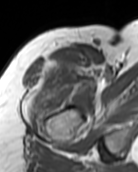
MRI of an extremity soft-tissue mass, one axial slice; position 82 of 99 along the scan axis; MR volume resampled by the dataset authors to the PET/CT grid (not the native acquisition matrix); 3.27 mm slice thickness; 138 × 172 image matrix. Female patient. From the clinical record (not read from this slice): histological type: pleiomorphic undifferentiated sarcoma; grade: high; site of the primary tumour: right quadricep.
Outlined on this slice (expert contour drawn on MRI and transferred to this co-registered scan by the dataset authors):
- gross tumour volume including surrounding oedema: bounding box [x1, y1, x2, y2] px = [28, 59, 90, 122]